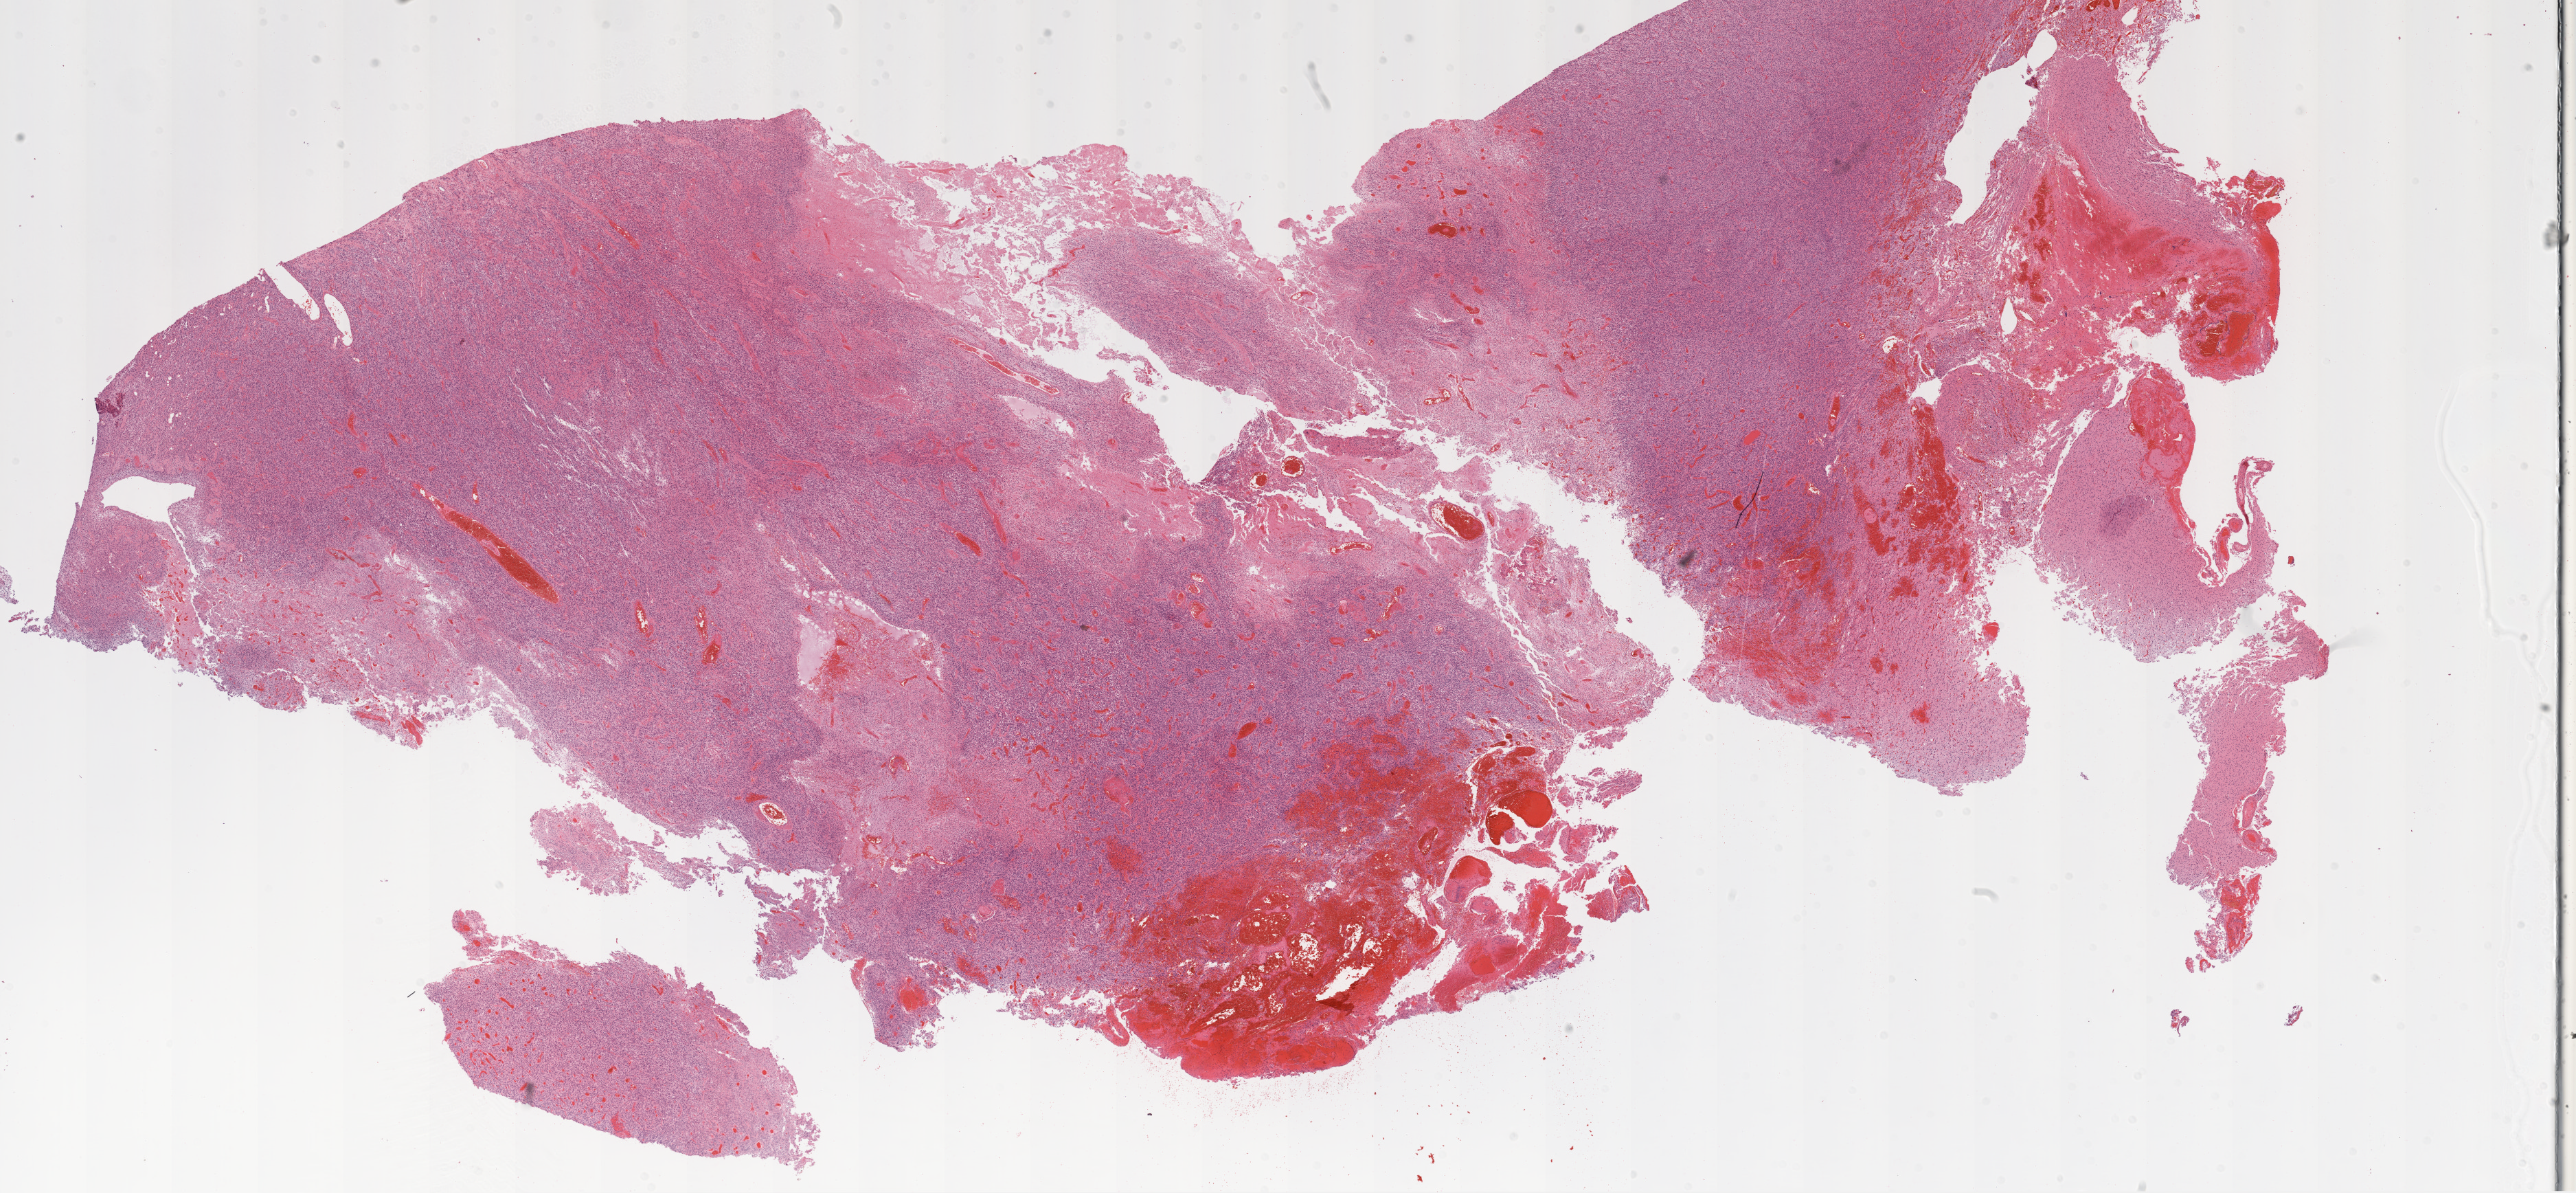
Digitized H&E tissue section (whole slide) — whole scanned area (about 30.1 x 13.9 mm, acquisition: 20x scan) shown as a low-resolution overview; formalin-fixed paraffin-embedded (FFPE) diagnostic section; sample: primary tumour, brain. Female patient; age at initial diagnosis 63 years.
- histologic diagnosis: Glioblastoma